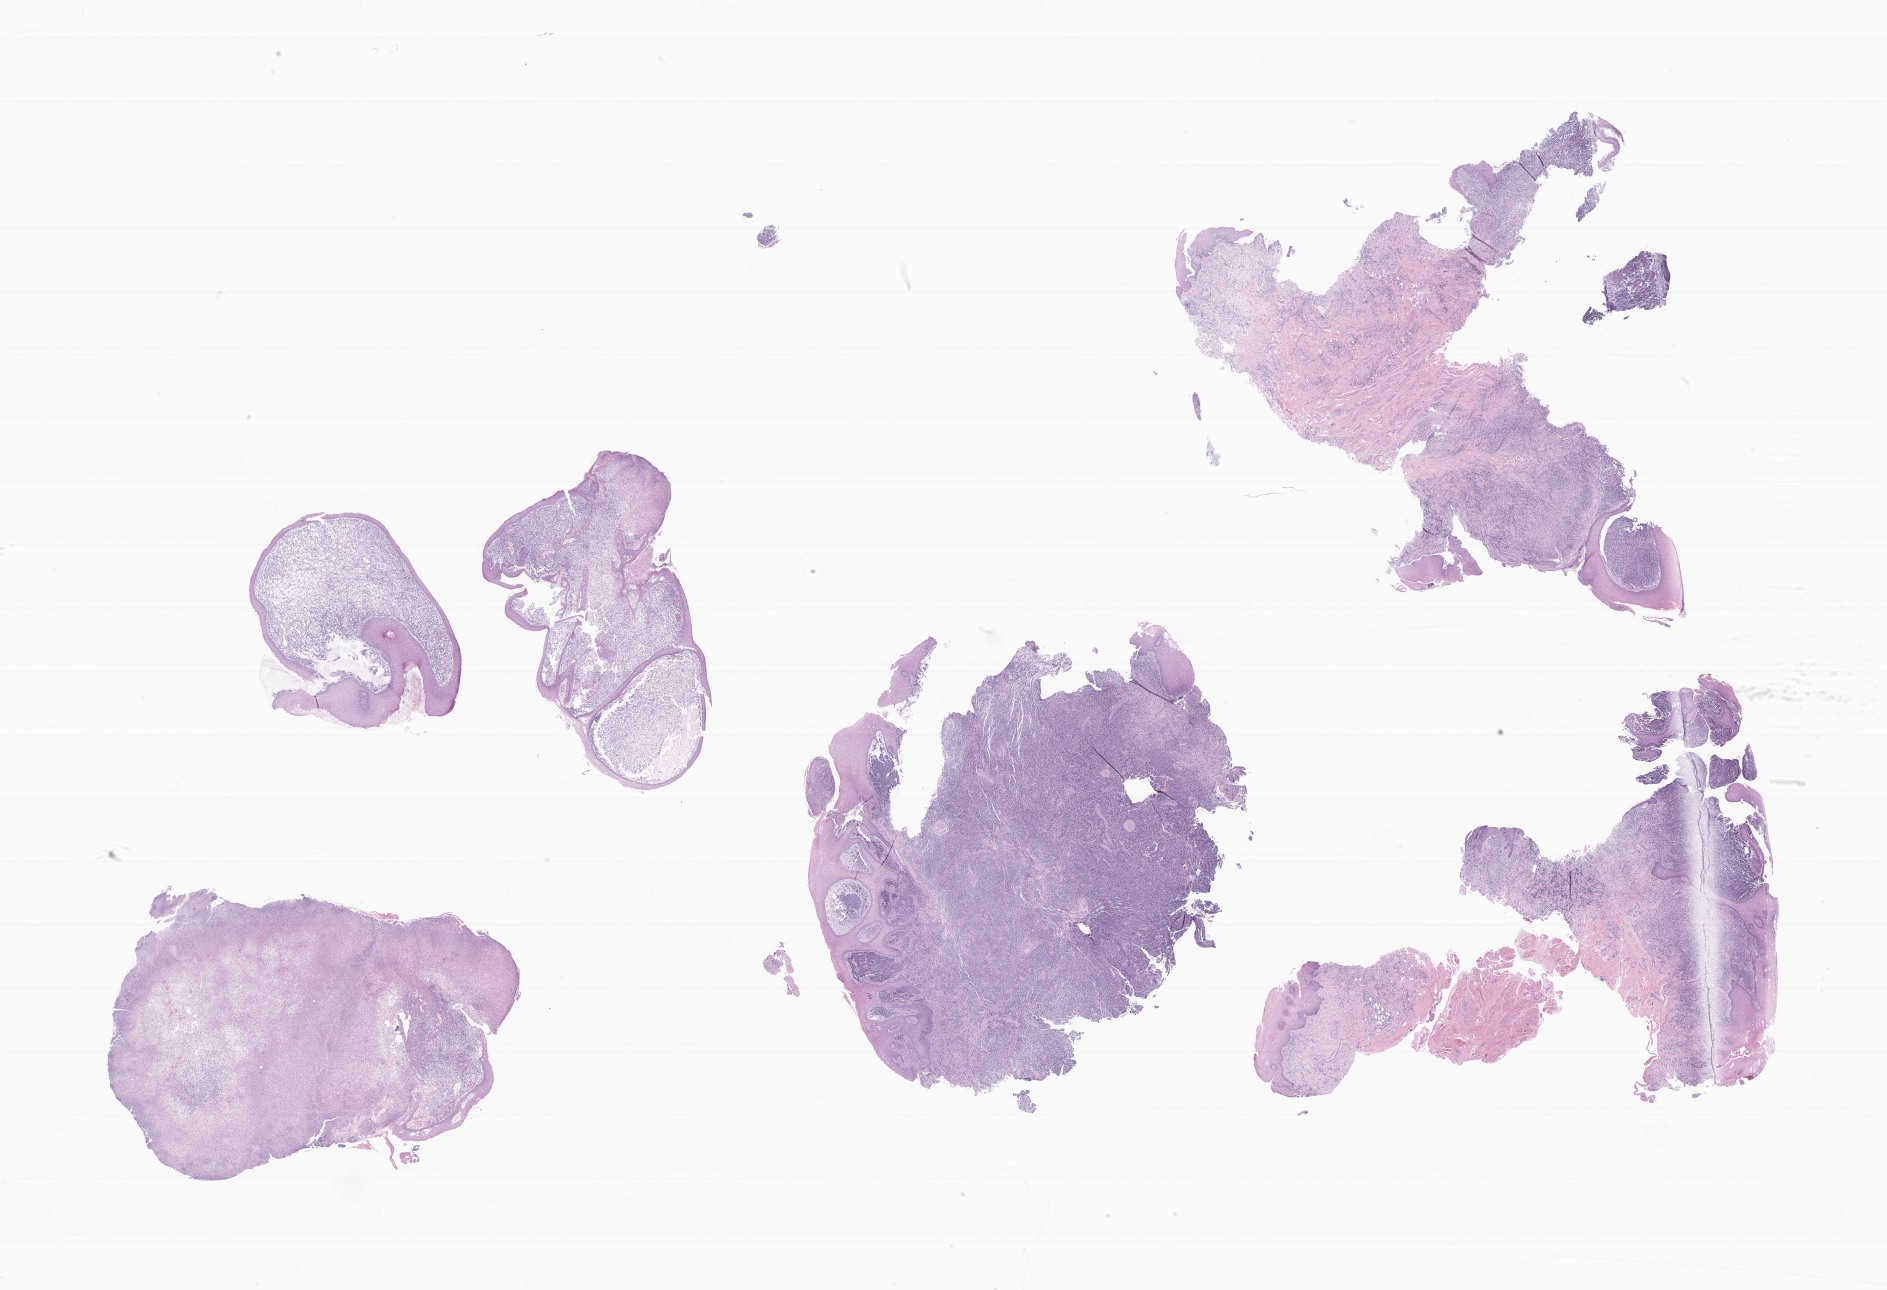
Digitized haematoxylin and eosin-stained section of tumor tissue from the buccal mucosa — low-resolution overview of the scanned area, about 31.8 x 21.8 mm, formalin-fixed, paraffin-embedded (FFPE) tissue. Patient female; age 97 months (8 years 1 month).
- diagnosis: Embryonal rhabdomyosarcoma, NOS